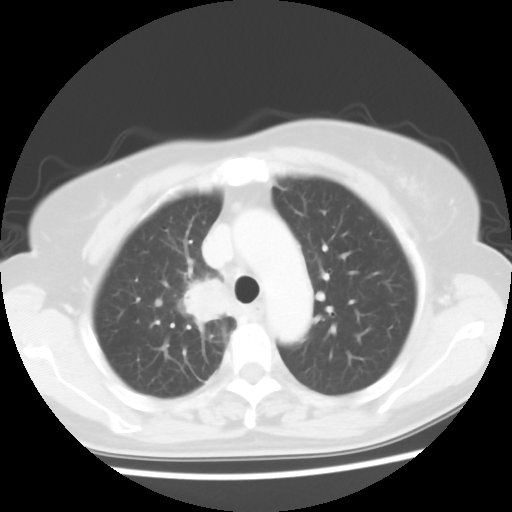
Chest CT, one axial slice. Position 42 of 56 along the scan axis. 120 kVp. Lung window (W 1500 / L -600 HU). 5 mm slice thickness. 512 × 512 image matrix, field of view 314 × 314 mm. Patient: female, 62 years. From the clinical record (not read from this slice): clinical TNM (as recorded): T2 N1 M1a.
Annotated regions visible in this slice (bounding box drawn by a radiologist):
- lung tumour (recorded histology: adenocarcinoma): bounding box <179,268,239,324> (left, top, right, bottom; pixels)